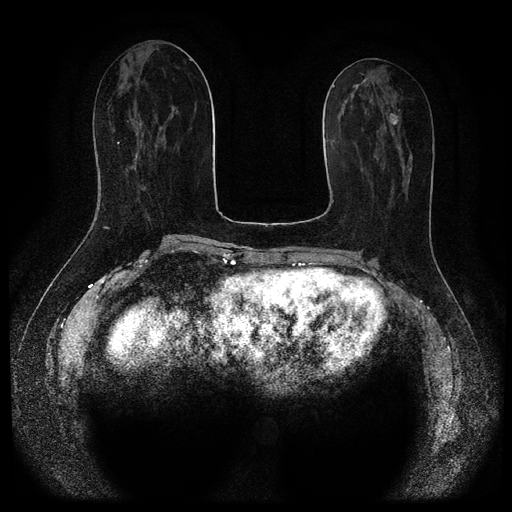
Breast MRI (dynamic contrast-enhanced, multi-phase), one axial slice; slice 42 of 116 in the series (ordered by position); dynamic contrast-enhanced series, time point 2 of 5 at this slice position (early post-contrast); 1.5 T; TE 2.7 ms, TR 5.4 ms; 2 mm slice thickness; 512 × 512 image matrix, field of view 340 × 340 mm. Female patient, age 47 years.
Structures marked on this image (semi-automatically segmented with operator editing):
- breast lesion (labelled benign in the annotation): bounding box [x1, y1, x2, y2] px = [389, 113, 399, 125]